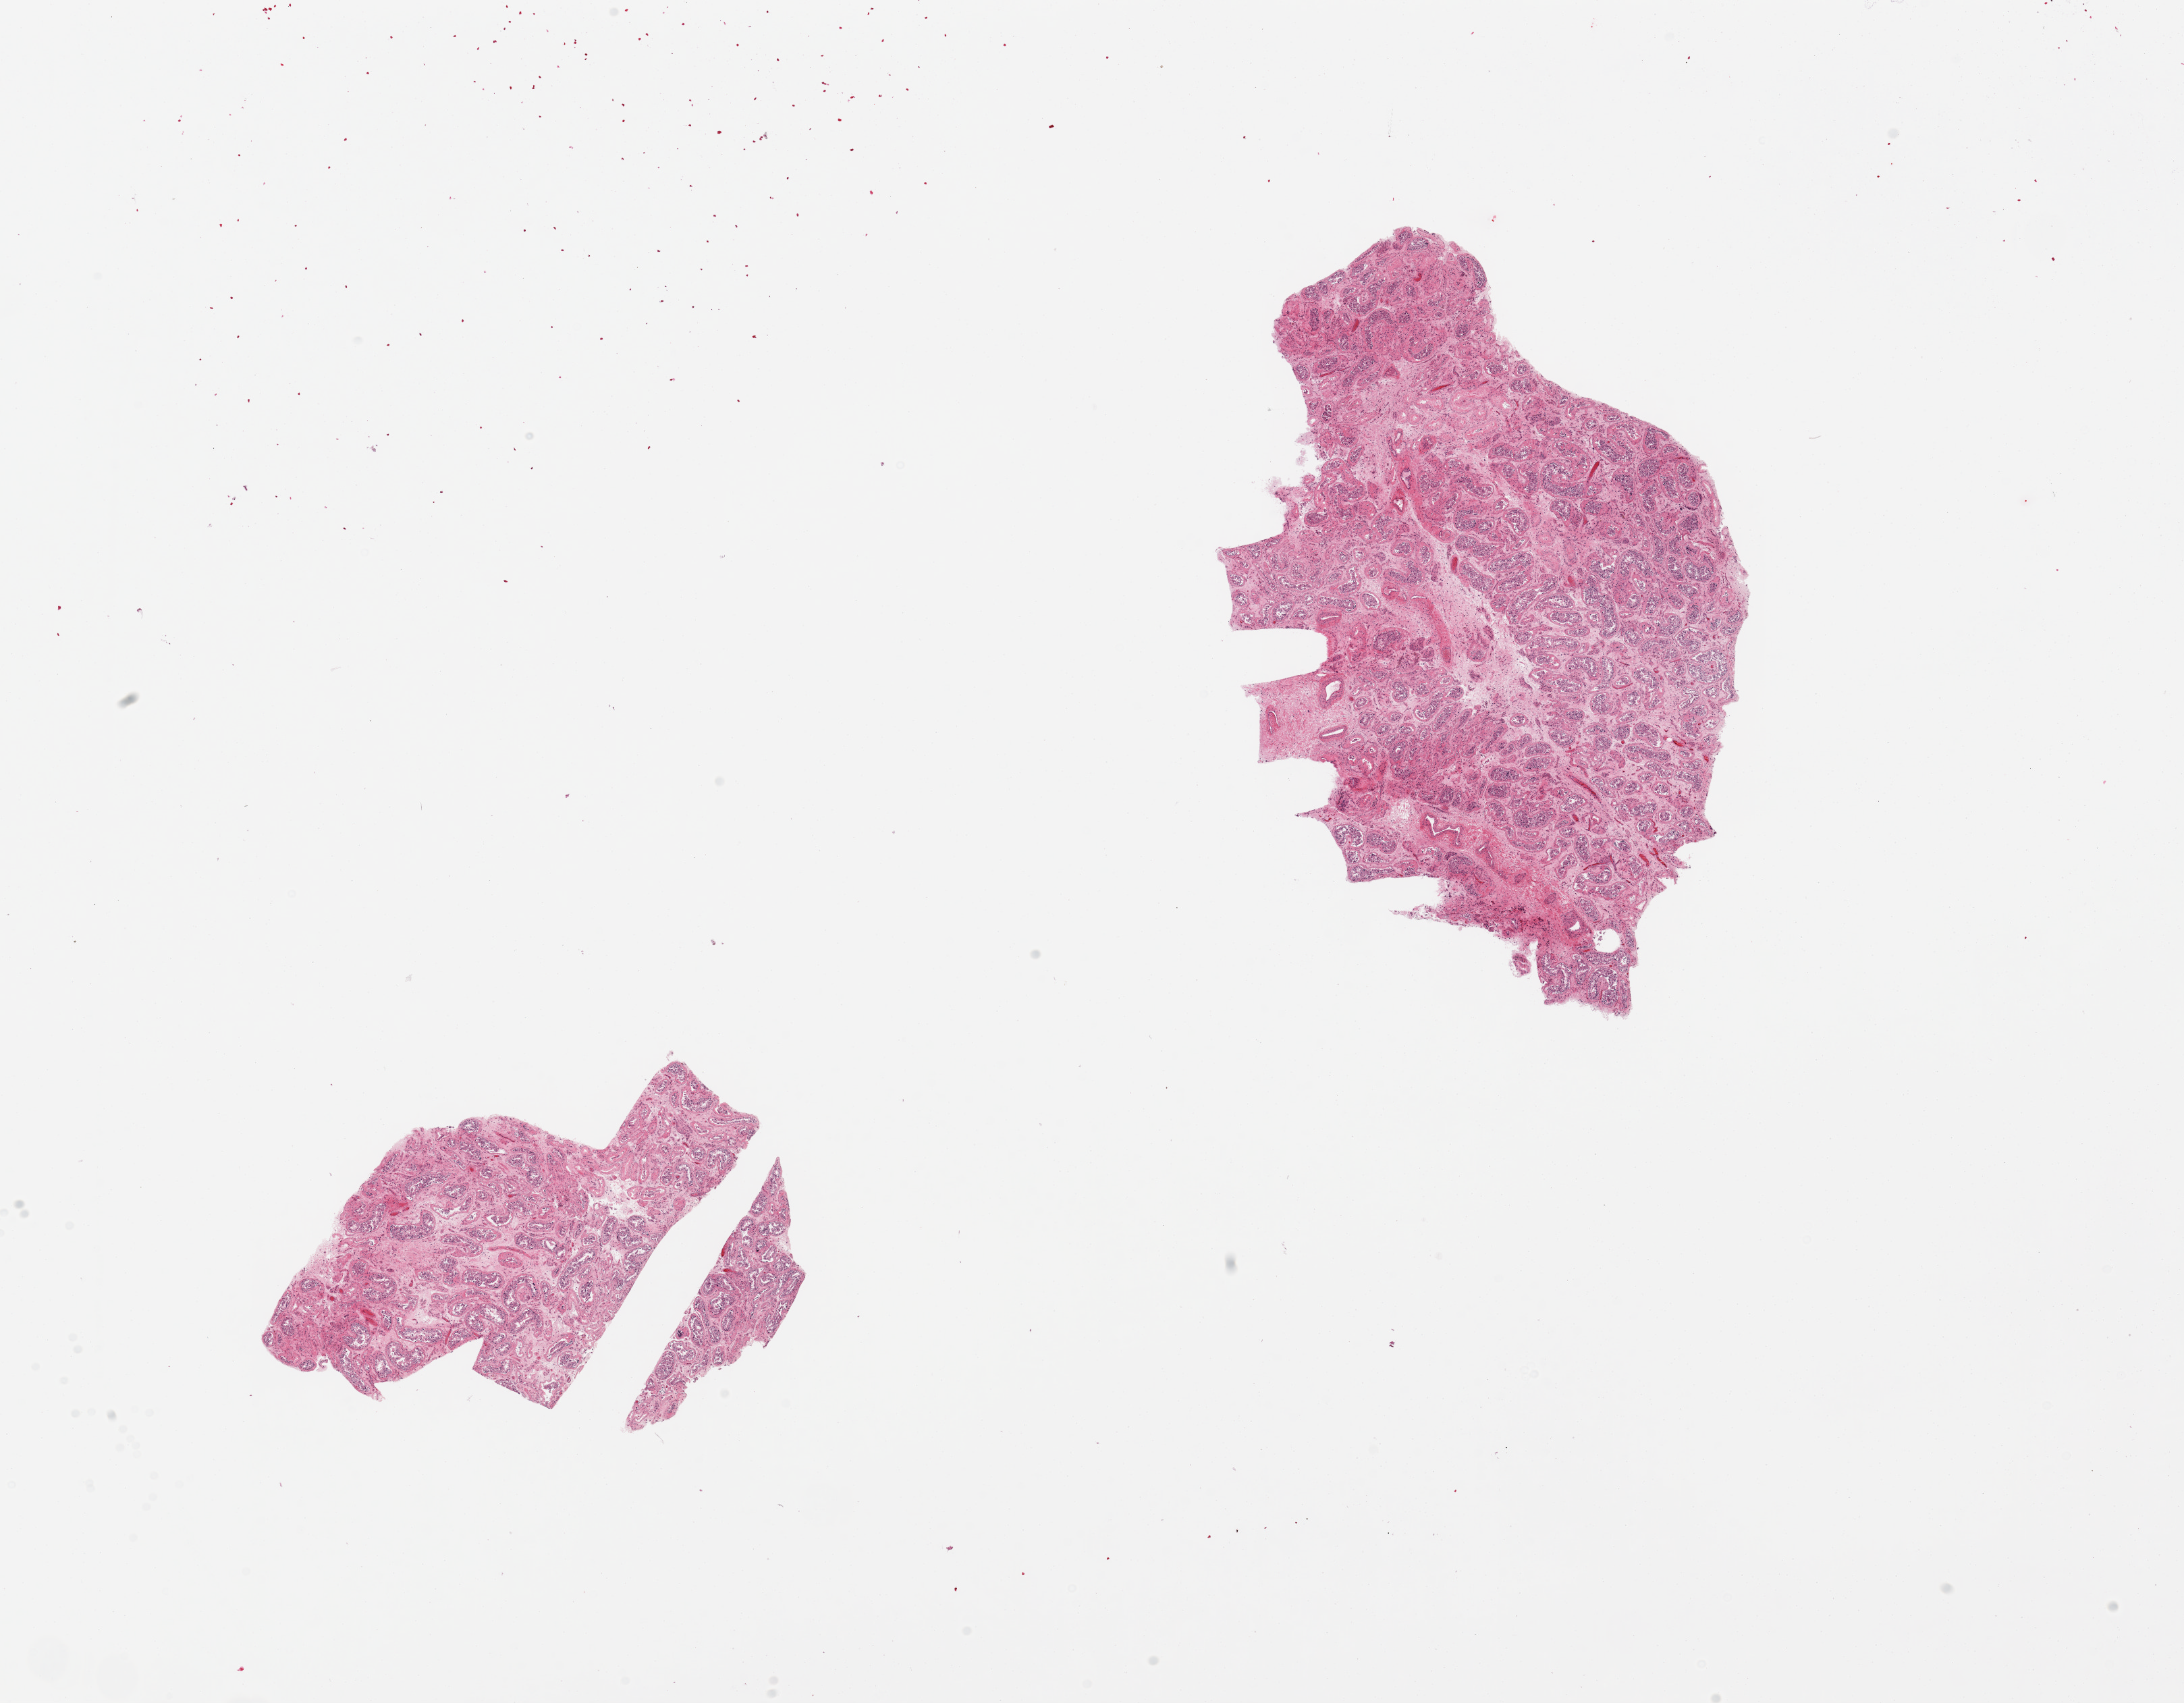
Whole-slide image, H&E stain — whole scanned area (about 25.6 x 20.0 mm) shown as a low-resolution overview, PAXgene-fixed, paraffin-embedded tissue, target tissue: testis, tissue donor sample. Donor sex: male.
Review note (as recorded): 2 pieces, diffuse atrophy/interstitial fibrosis. Tubules badly autolyzed, spermatogenesis appears reduced/absent.